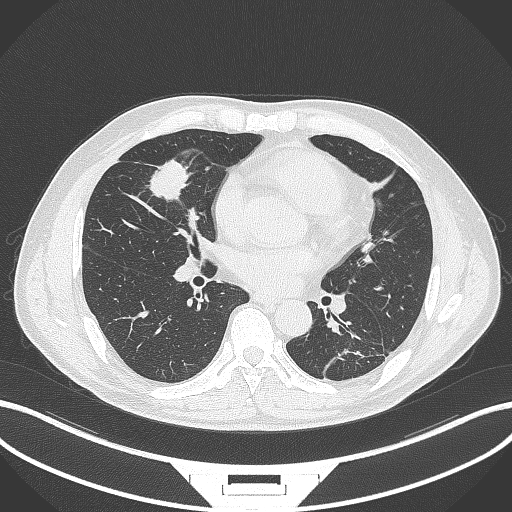
Chest CT, one axial slice. Position 140 of 399 along the scan axis. Lung window (W 1500 / L -600 HU). 1 mm slice thickness. 512 × 512 image matrix, field of view 400 × 400 mm. Male patient, age 59 years. Case-level facts recorded for this patient, not image findings: clinical TNM (as recorded): T2a N1 M0.
Annotated regions visible in this slice (rectangle marked by the reading radiologist):
- lung tumour (recorded histology: adenocarcinoma): box from (x=147, y=159) to (x=191, y=205) px